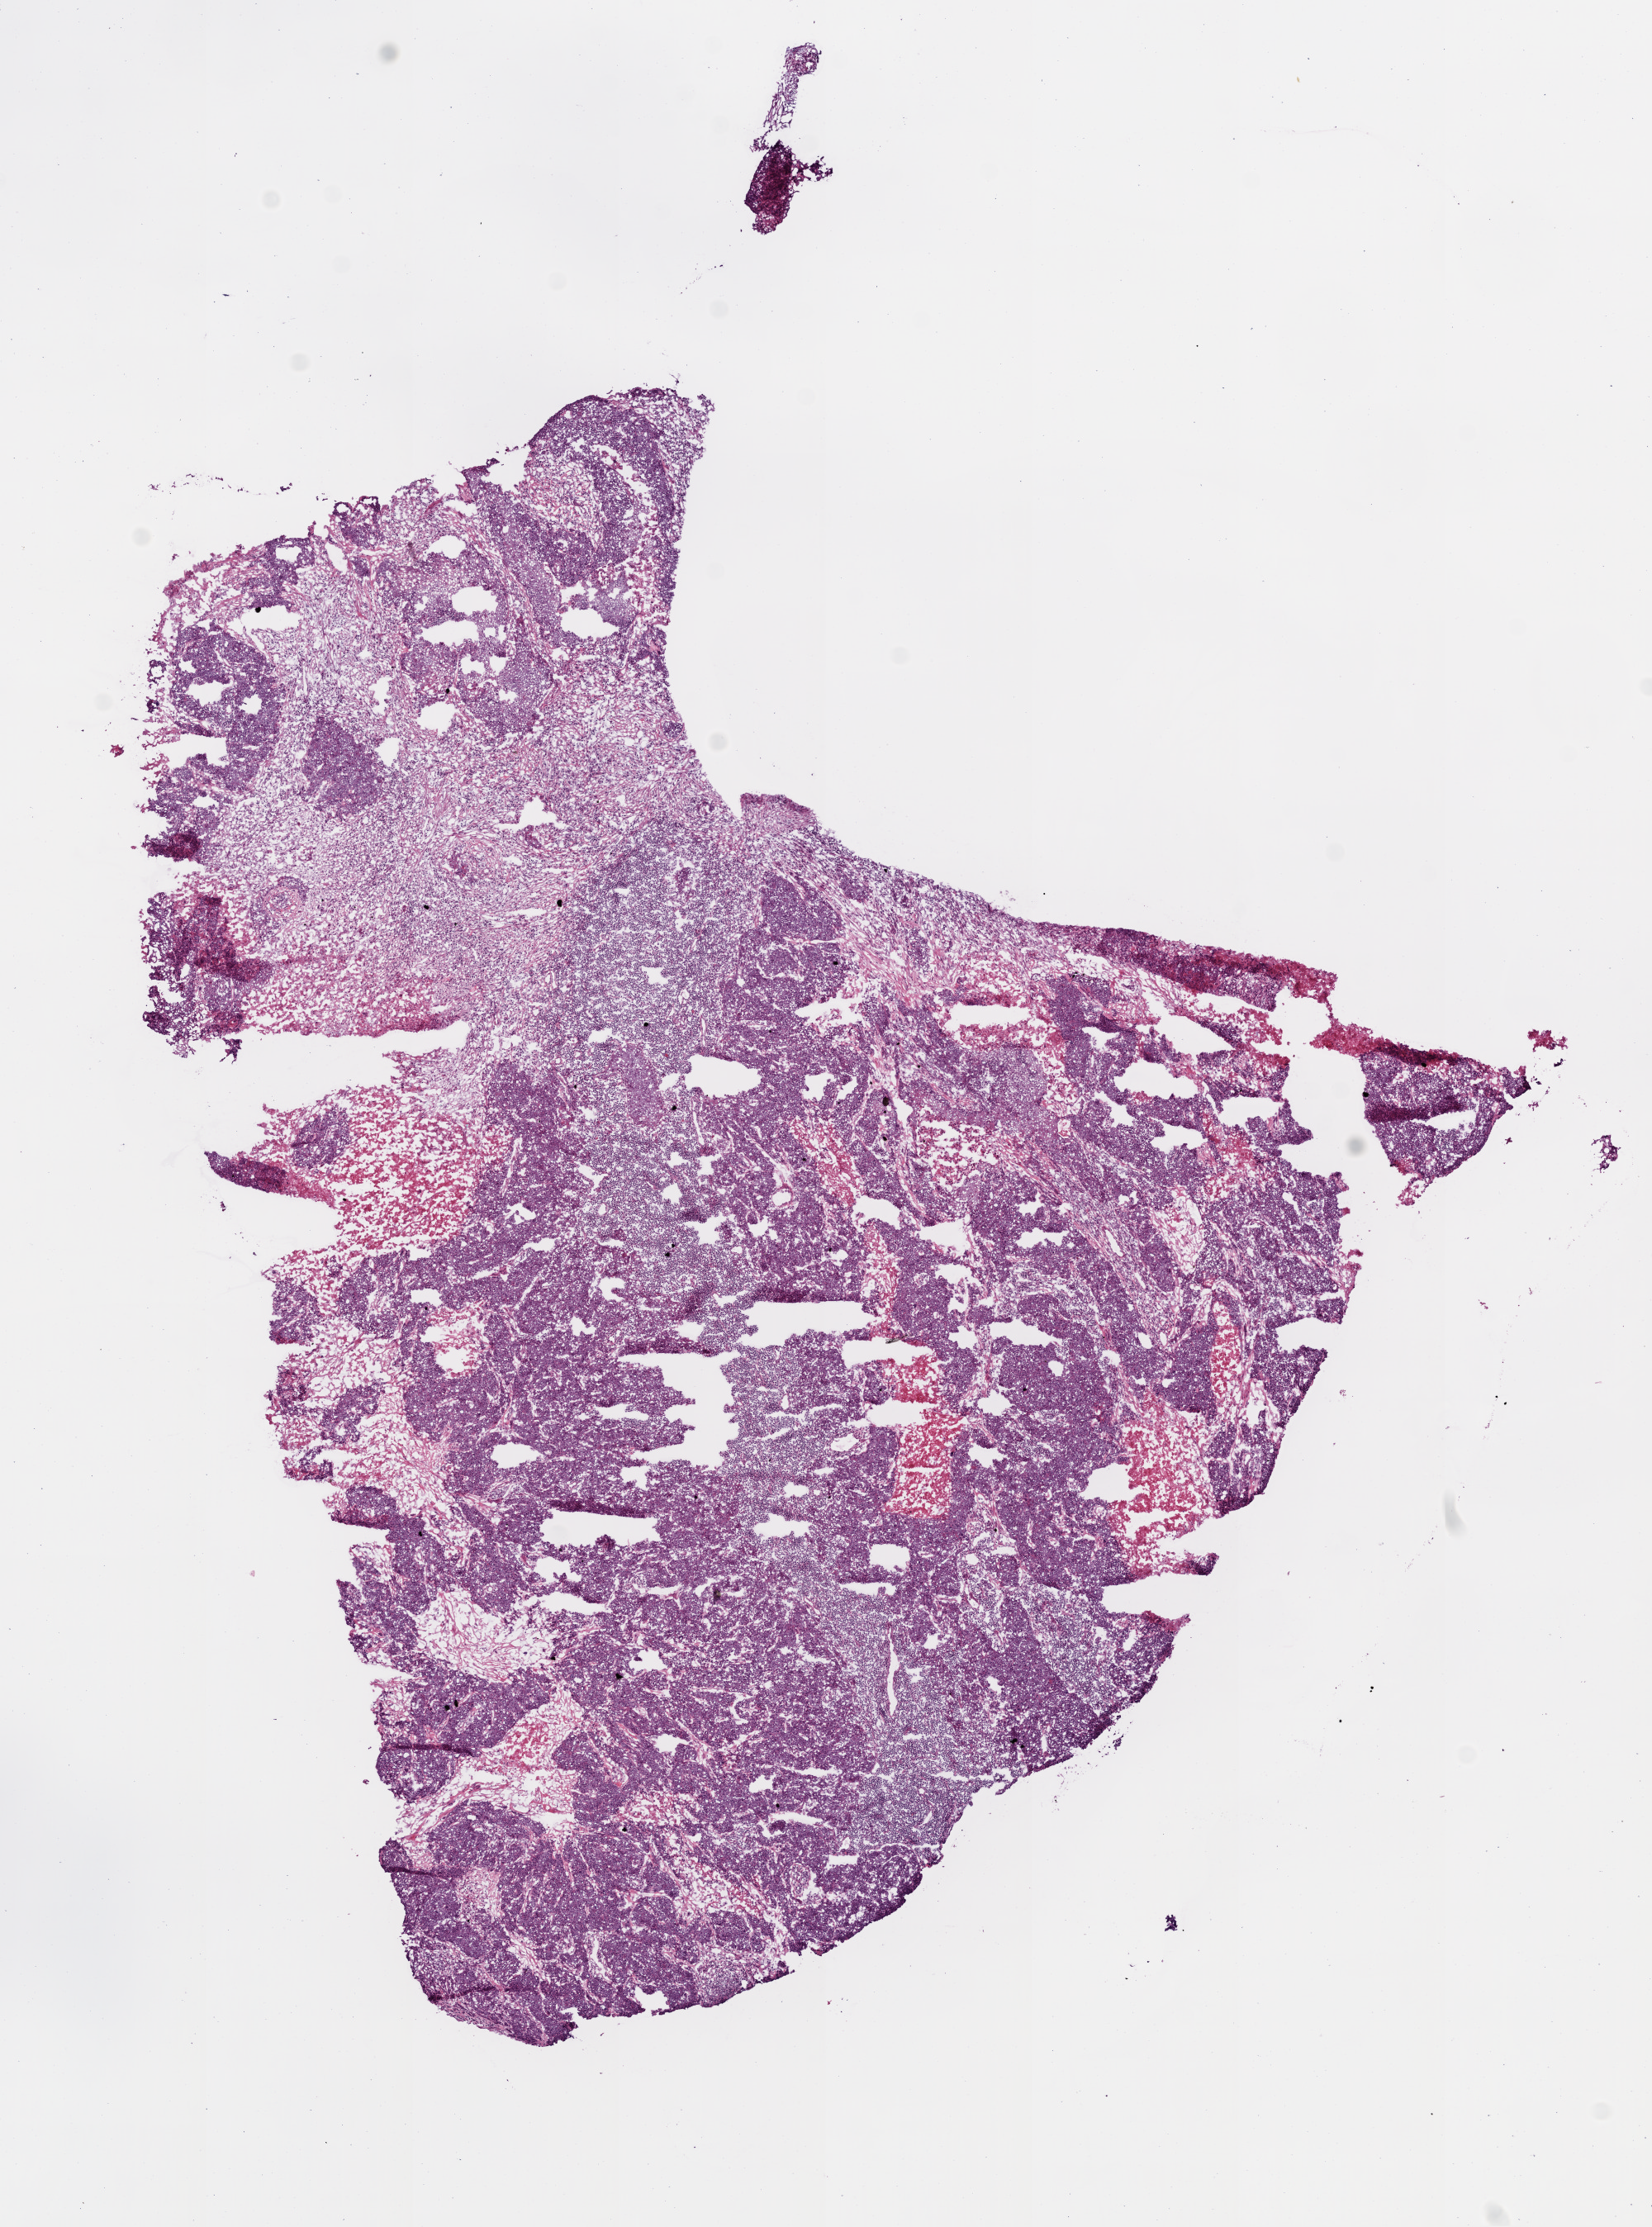
H&E-stained whole-slide image, whole scanned area (about 8.0 x 10.8 mm, acquisition: 20x scan) shown as a low-resolution overview; frozen section from the bottom of the tissue portion; primary tumour sample from the head and neck. Patient: male, age at initial diagnosis 48 years. Histologic grade: G3 (poorly differentiated). Slide review estimates, as recorded: tumour cells 80%, tumour nuclei 72%, stromal cells 10%, necrosis 10%. Inflammatory infiltration, as recorded: lymphocyte infiltration 10%.
* histologic diagnosis: Squamous cell carcinoma, NOS (tonsil, NOS)
* AJCC pathologic stage: IVA (7th edition)
* laterality: left
* TNM: T2 N2b M0